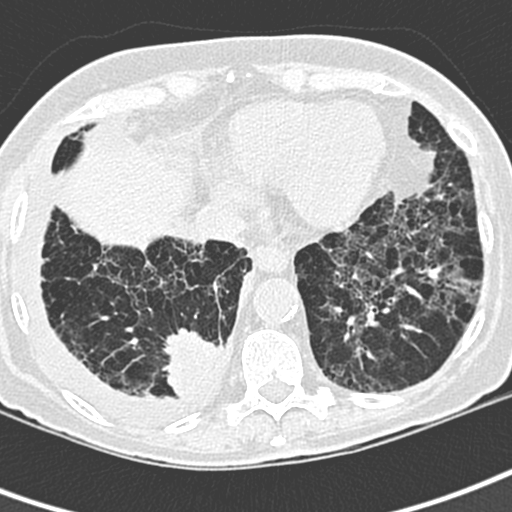
Low-dose screening chest CT, one axial slice; position 77 of 220 along the scan axis; 120 kVp; lung window (W 1500 / L -600 HU); 512 × 512 image matrix, field of view 288 × 288 mm.
Annotated regions visible in this slice (manually delineated by an expert):
- lesion 1 (tumor, lower lobe of right lung): bounding box (x1, y1, x2, y2) in pixels: (164, 329, 222, 397)